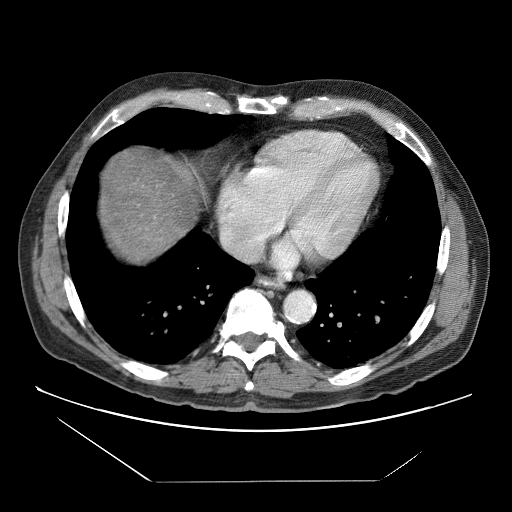
Contrast-enhanced abdominal CT (liver protocol), one axial slice. Position 72 of 83 along the scan axis. Reconstruction kernel STANDARD. 120 kVp. Soft-tissue window (W 400 / L 40 HU). 2.5 mm slice thickness. 512 × 512 image matrix. From the clinical record (not read from this slice): diagnosis: hepatocellular carcinoma (patient treated with transarterial chemoembolisation; whether this scan precedes or follows treatment is not stated here); TNM stage (as recorded): Stage-IVB; Child-Pugh class: B; tumour differentiation: poorly differentiated; tumour nodularity: uninodular.
Structures marked on this image (semi-automatic segmentation, software-assisted and operator-edited):
- abdominal aorta: box from (x=285, y=292) to (x=313, y=321) px
- liver parenchyma outside the tumour (the mass and vessels are separate outlines, so this box may not span the whole liver): (x=100, y=146)–(x=204, y=260)